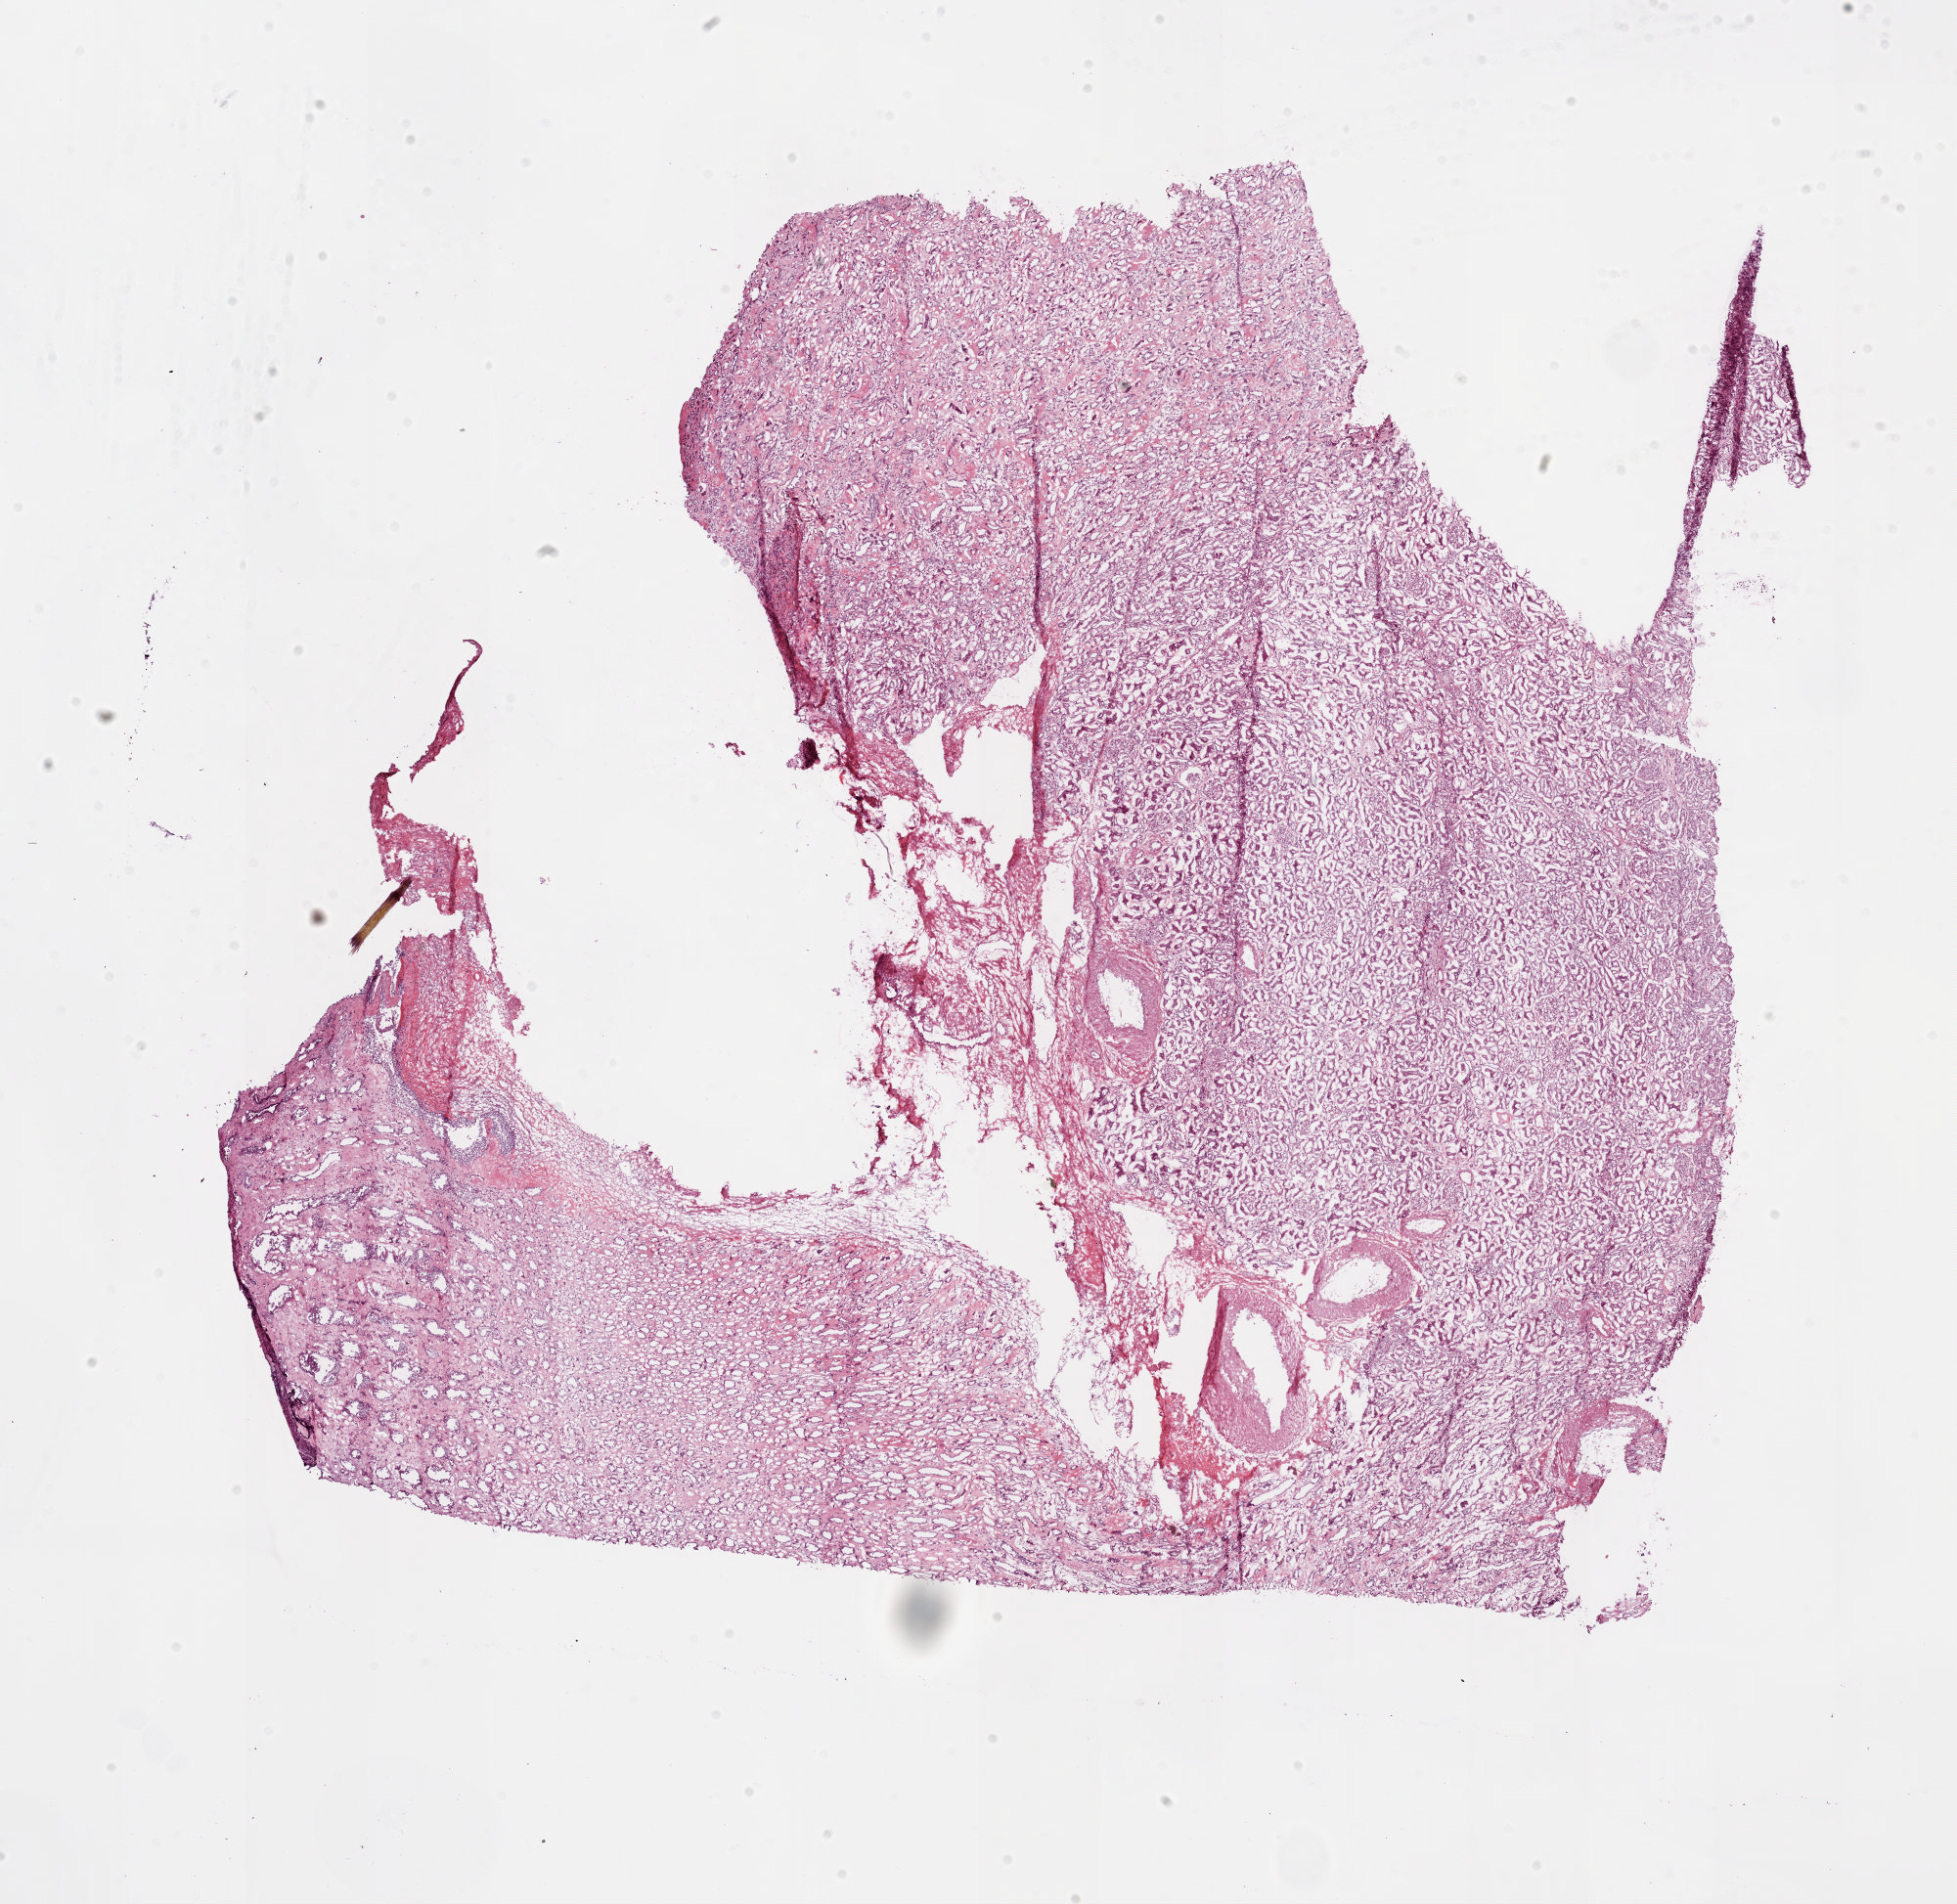
H&E-stained whole-slide image — a low-resolution overview of the entire scanned area, about 15.9 x 15.4 mm (slide scanned at 20x); frozen section from the bottom of the tissue portion; solid tissue normal (non-tumour tissue) sample from the kidney. Patient: male, age at initial diagnosis 72 years.
* this section: solid tissue normal sample (biorepository sample class)
* patient diagnosis: Clear cell adenocarcinoma, NOS